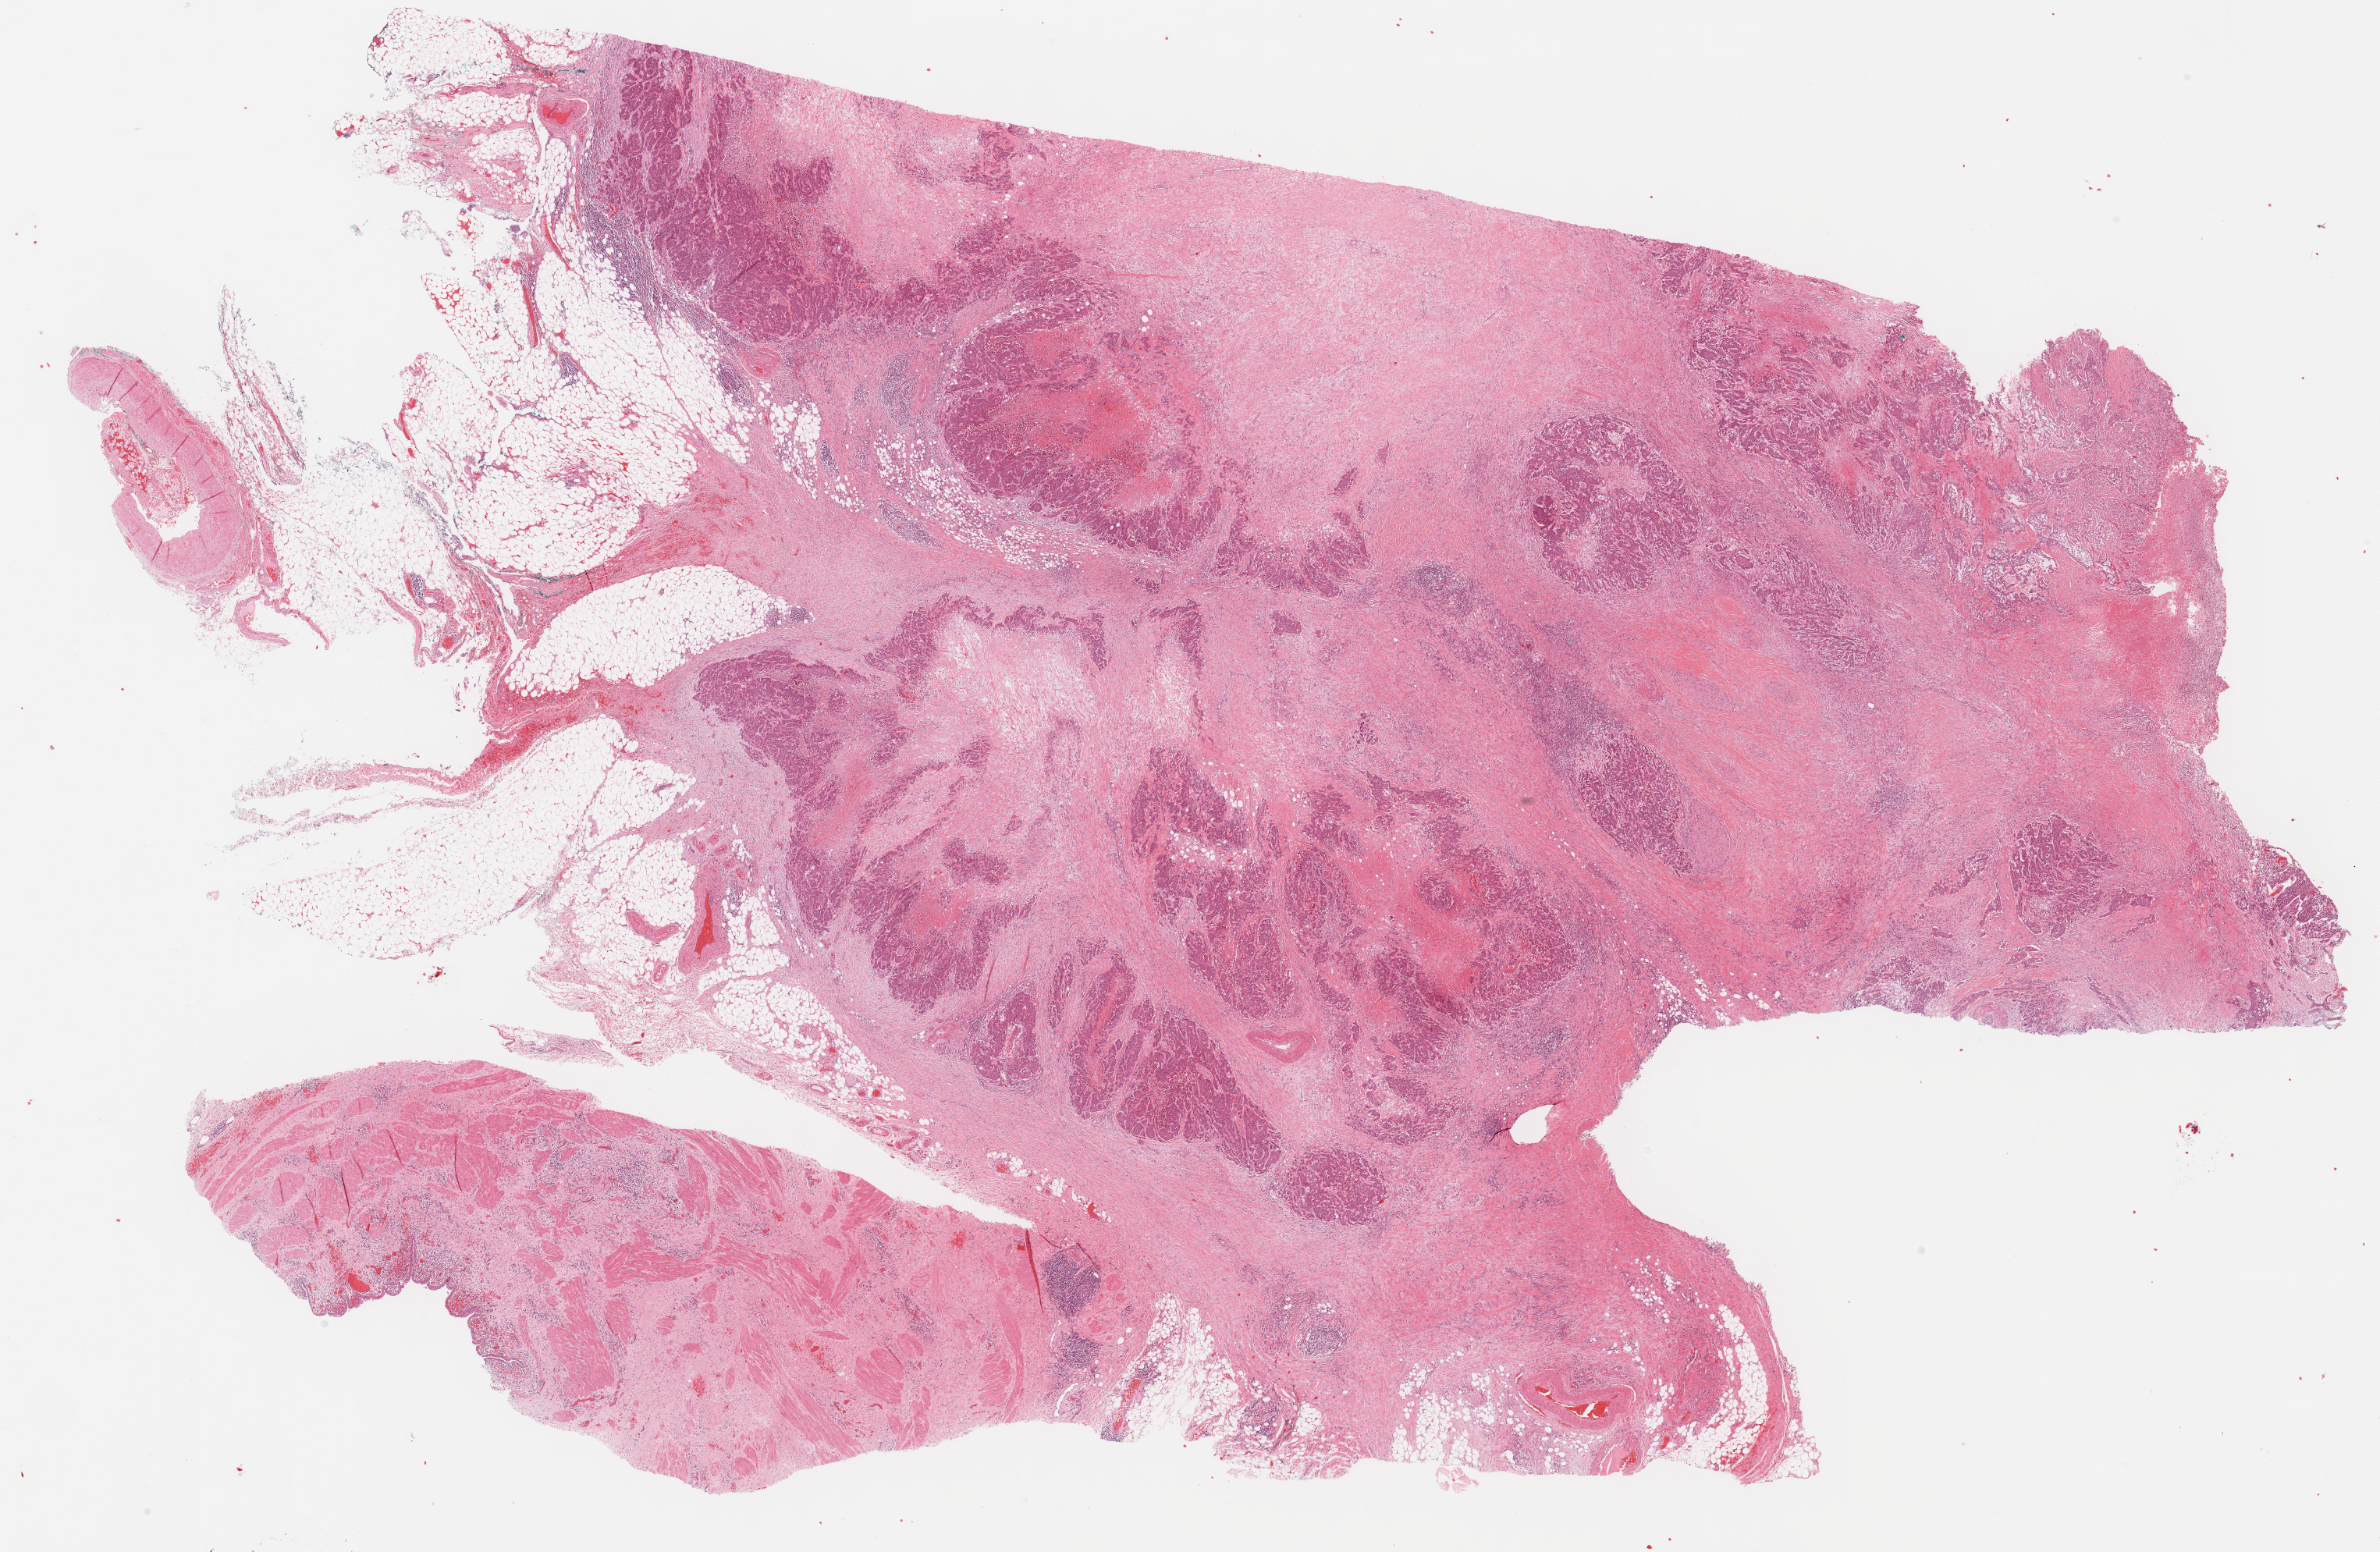
Digitized Hematoxylin and eosin (H&E) stained tissue section (whole slide), shown as a low-resolution overview of the whole scanned area (about 24.7 x 16.1 mm, from a 40x scan); formalin-fixed paraffin-embedded (FFPE) diagnostic section; bladder, primary tumour sample. Patient: male, age at initial diagnosis 56 years. Histologic grade: high grade.
• diagnosis: Transitional cell carcinoma
• lymph nodes positive (case pathology): 0 of 15 examined
• TNM: T3b N0 MX
• AJCC pathologic stage: III (6th edition)